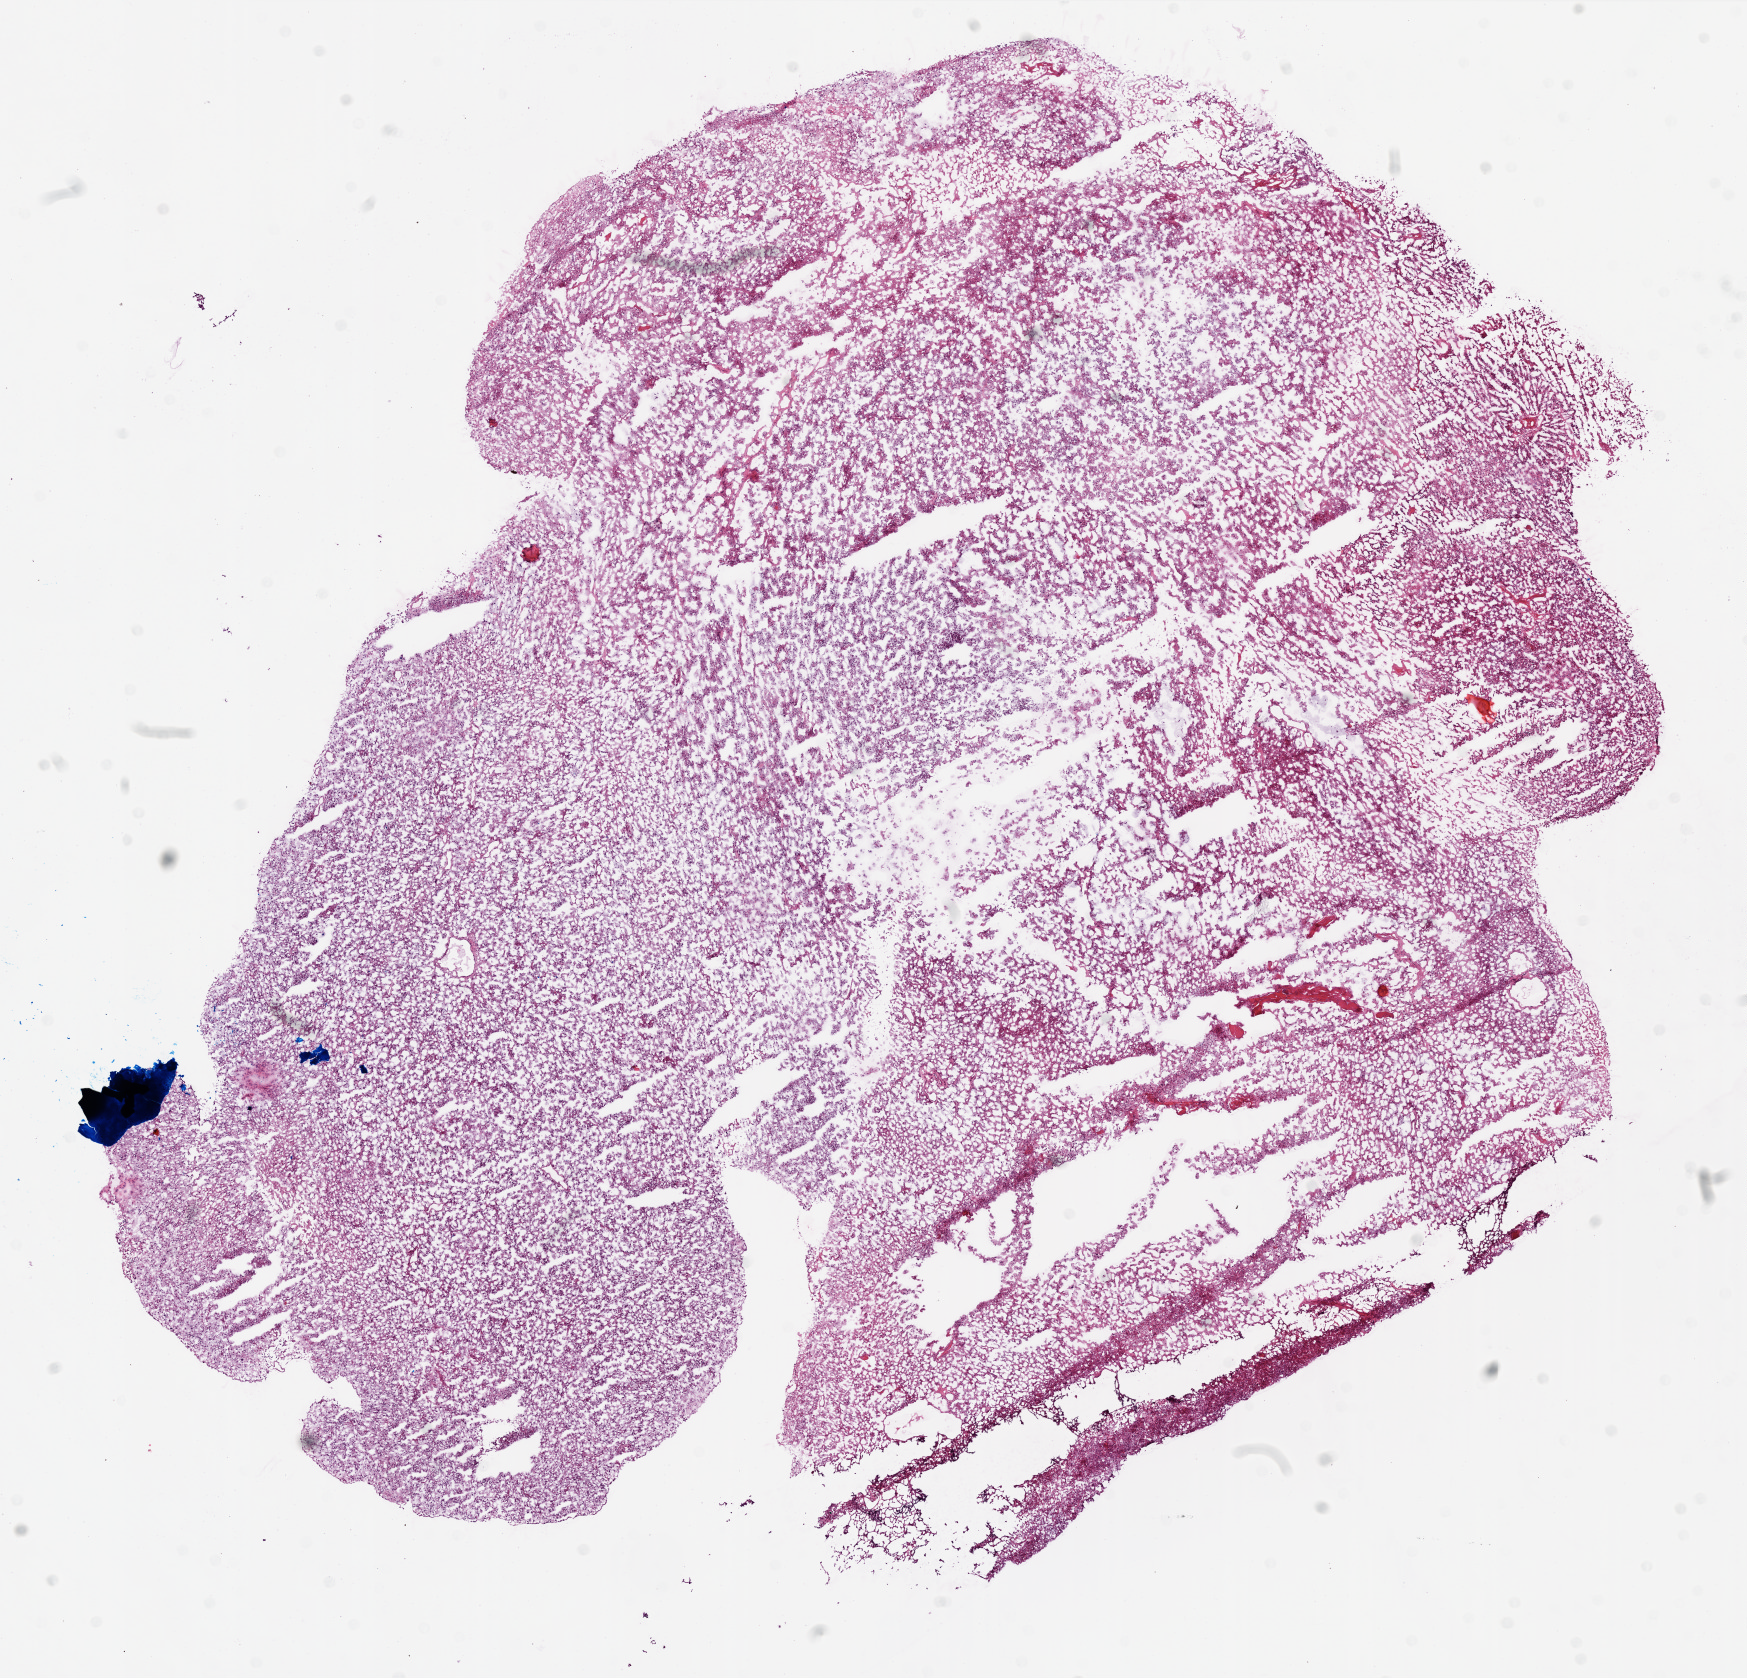
Digitized H&E-stained tissue section (whole slide), a low-resolution overview of the entire scanned area, about 14.0 x 13.4 mm. Slide review estimates, as recorded: tumour cells 75%, tumour nuclei 100%, normal cells 0%, stromal cells 0%, necrosis 25%.
Specimen: frozen section from the top of the tissue portion; sample: primary tumour, brain.